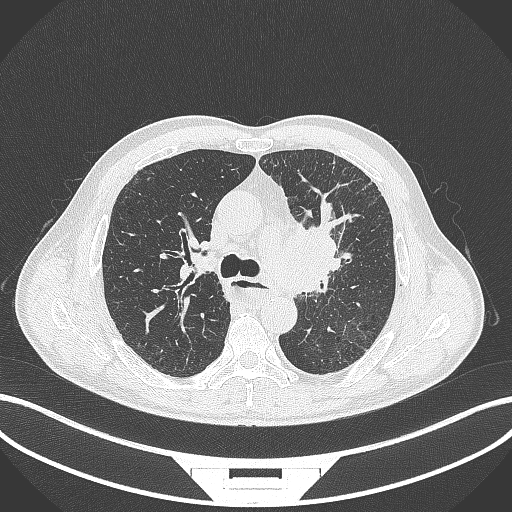
Chest CT, one axial slice; position 251 of 411 along the scan axis; reconstruction kernel B70f; 120 kVp; lung window (W 1500 / L -600 HU); 1 mm slice thickness; 512 × 512 image matrix. Patient: male, 57 years. Case-level facts recorded for this patient, not image findings: clinical TNM (as recorded): T2a N1 M0.
Annotated regions visible in this slice (rectangle marked by the reading radiologist):
- lung tumour (recorded histology: squamous cell carcinoma): bounding box <276,212,351,301> (left, top, right, bottom; pixels)